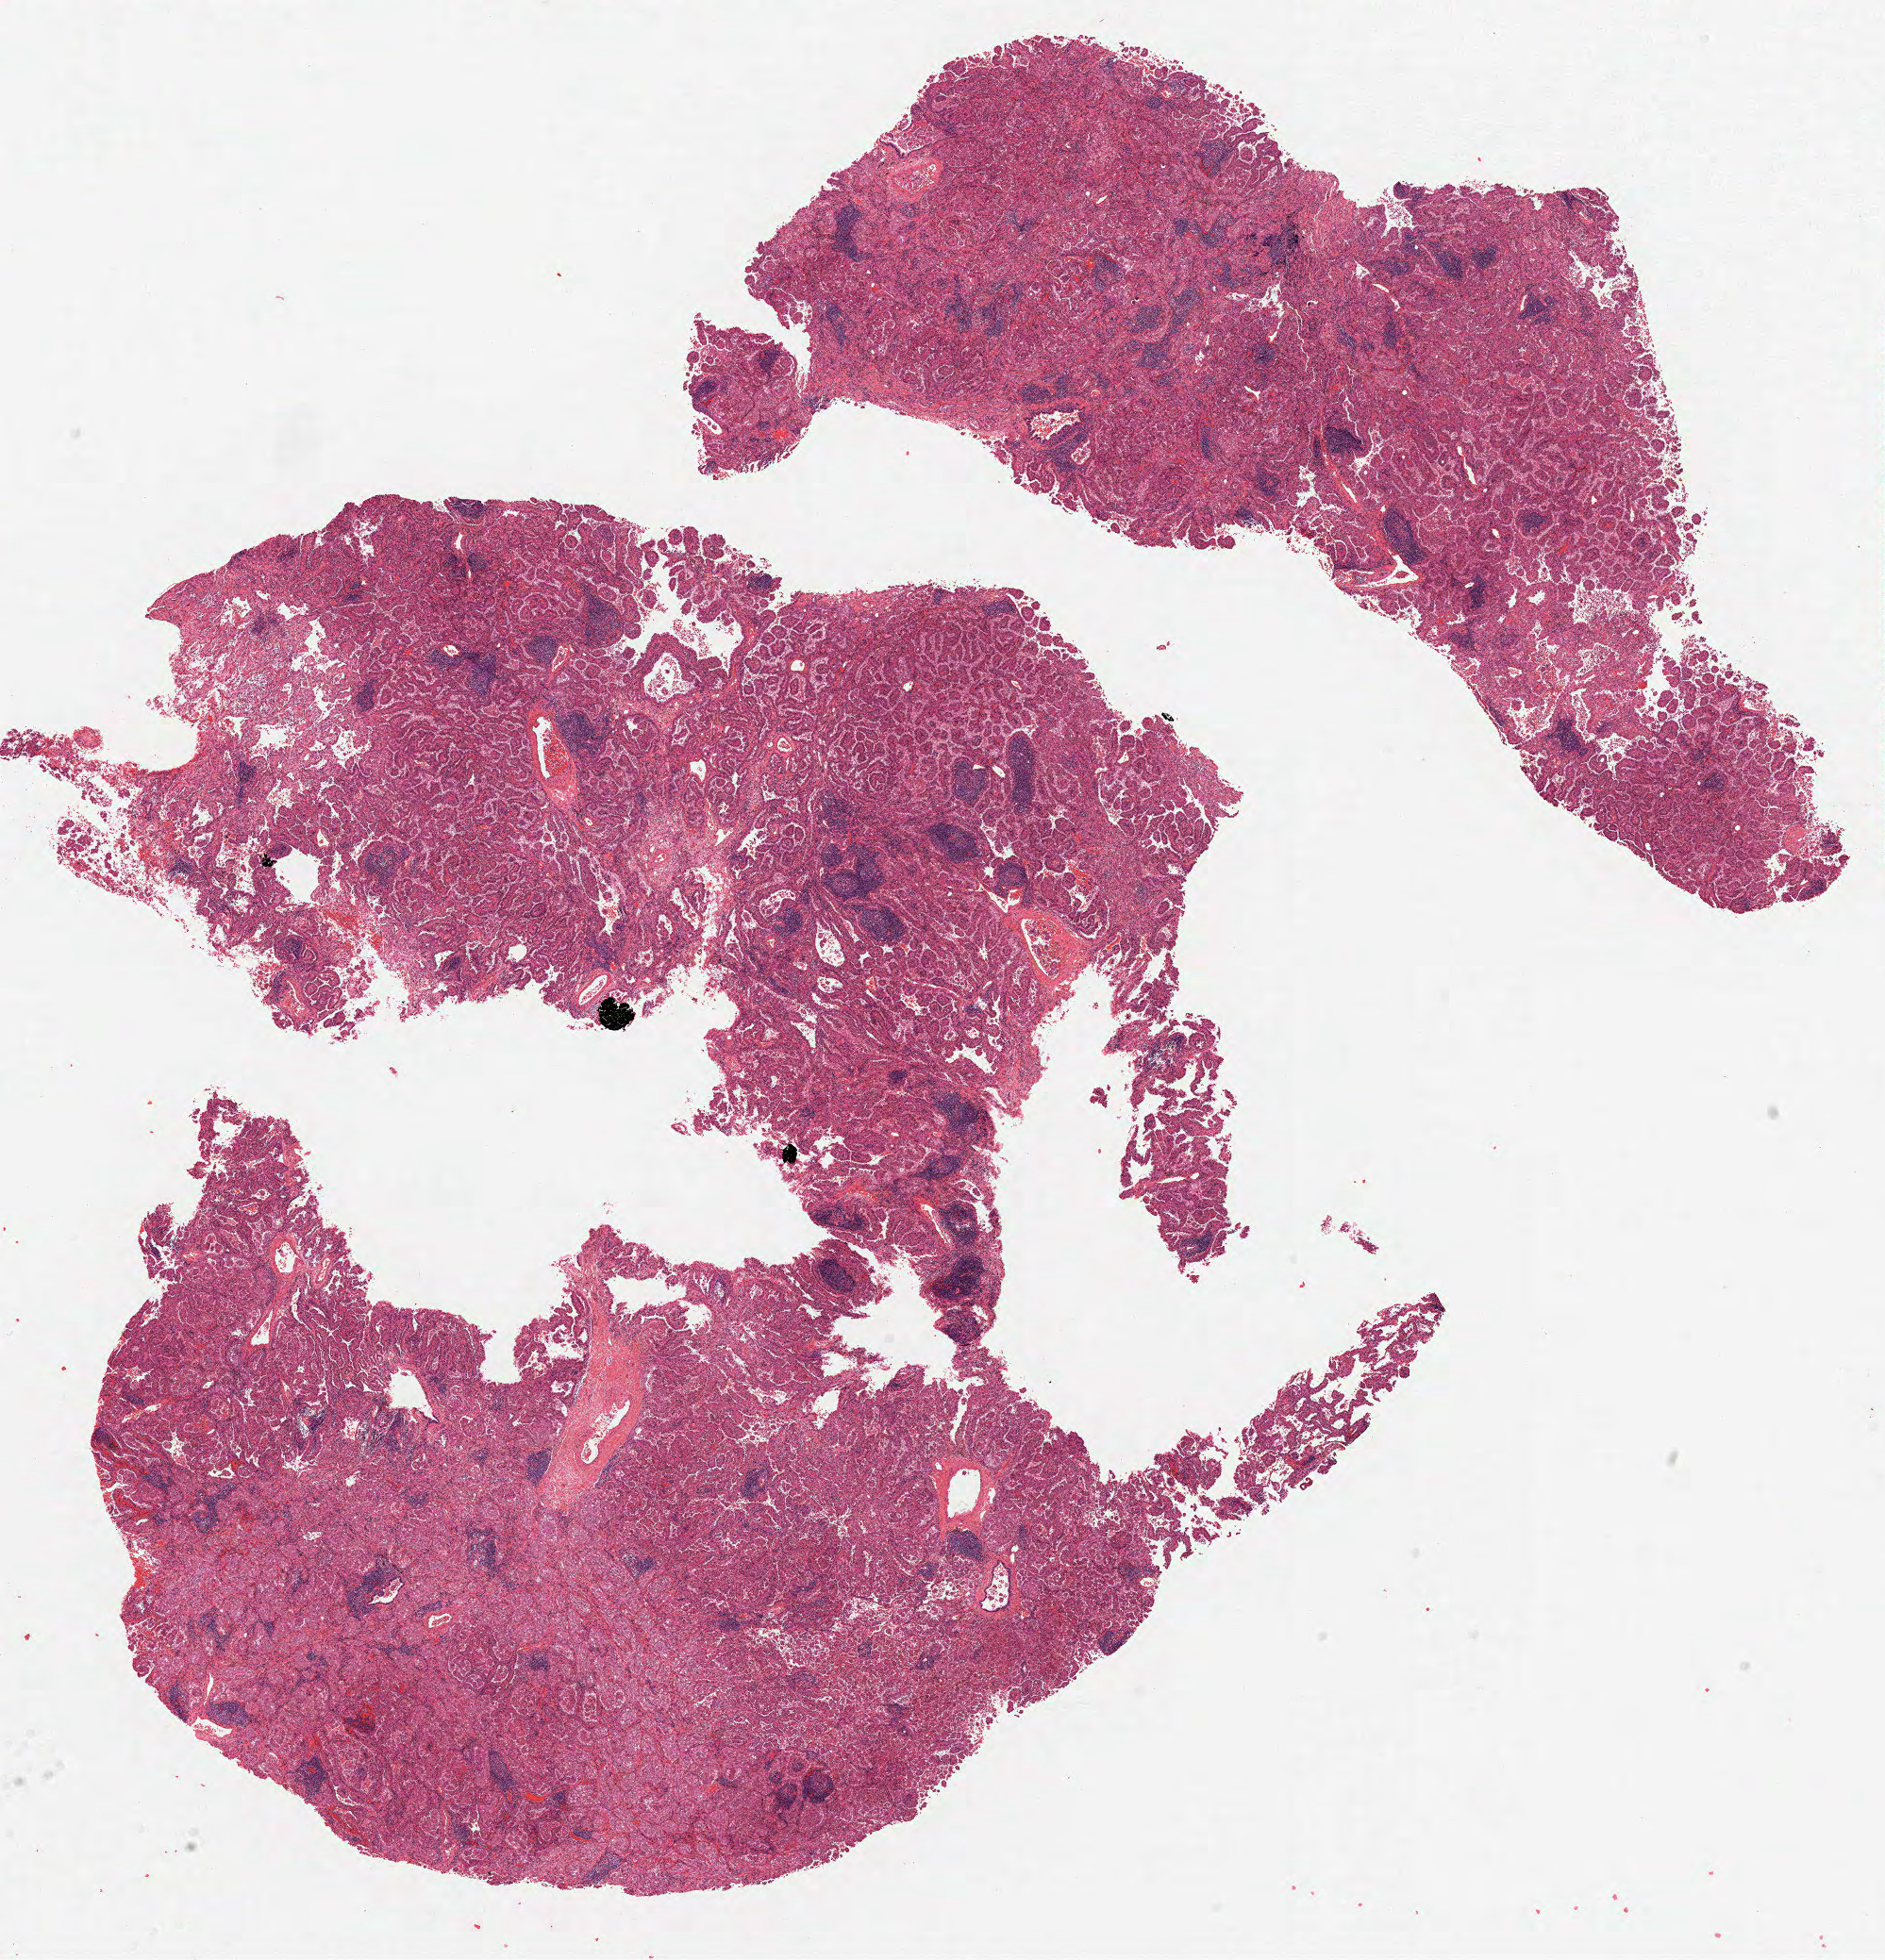
Whole-slide histology image, Hematoxylin and eosin (H&E) stained, a low-resolution overview of the entire scanned area, about 16.0 x 16.6 mm; formalin-fixed paraffin-embedded (FFPE) diagnostic section; lung, primary tumour sample. Patient sex: female.
AJCC pathologic stage: IIB (6th edition). Laterality: left. Histologic diagnosis: Invasive micropapillary carcinoma (lower lobe, lung).